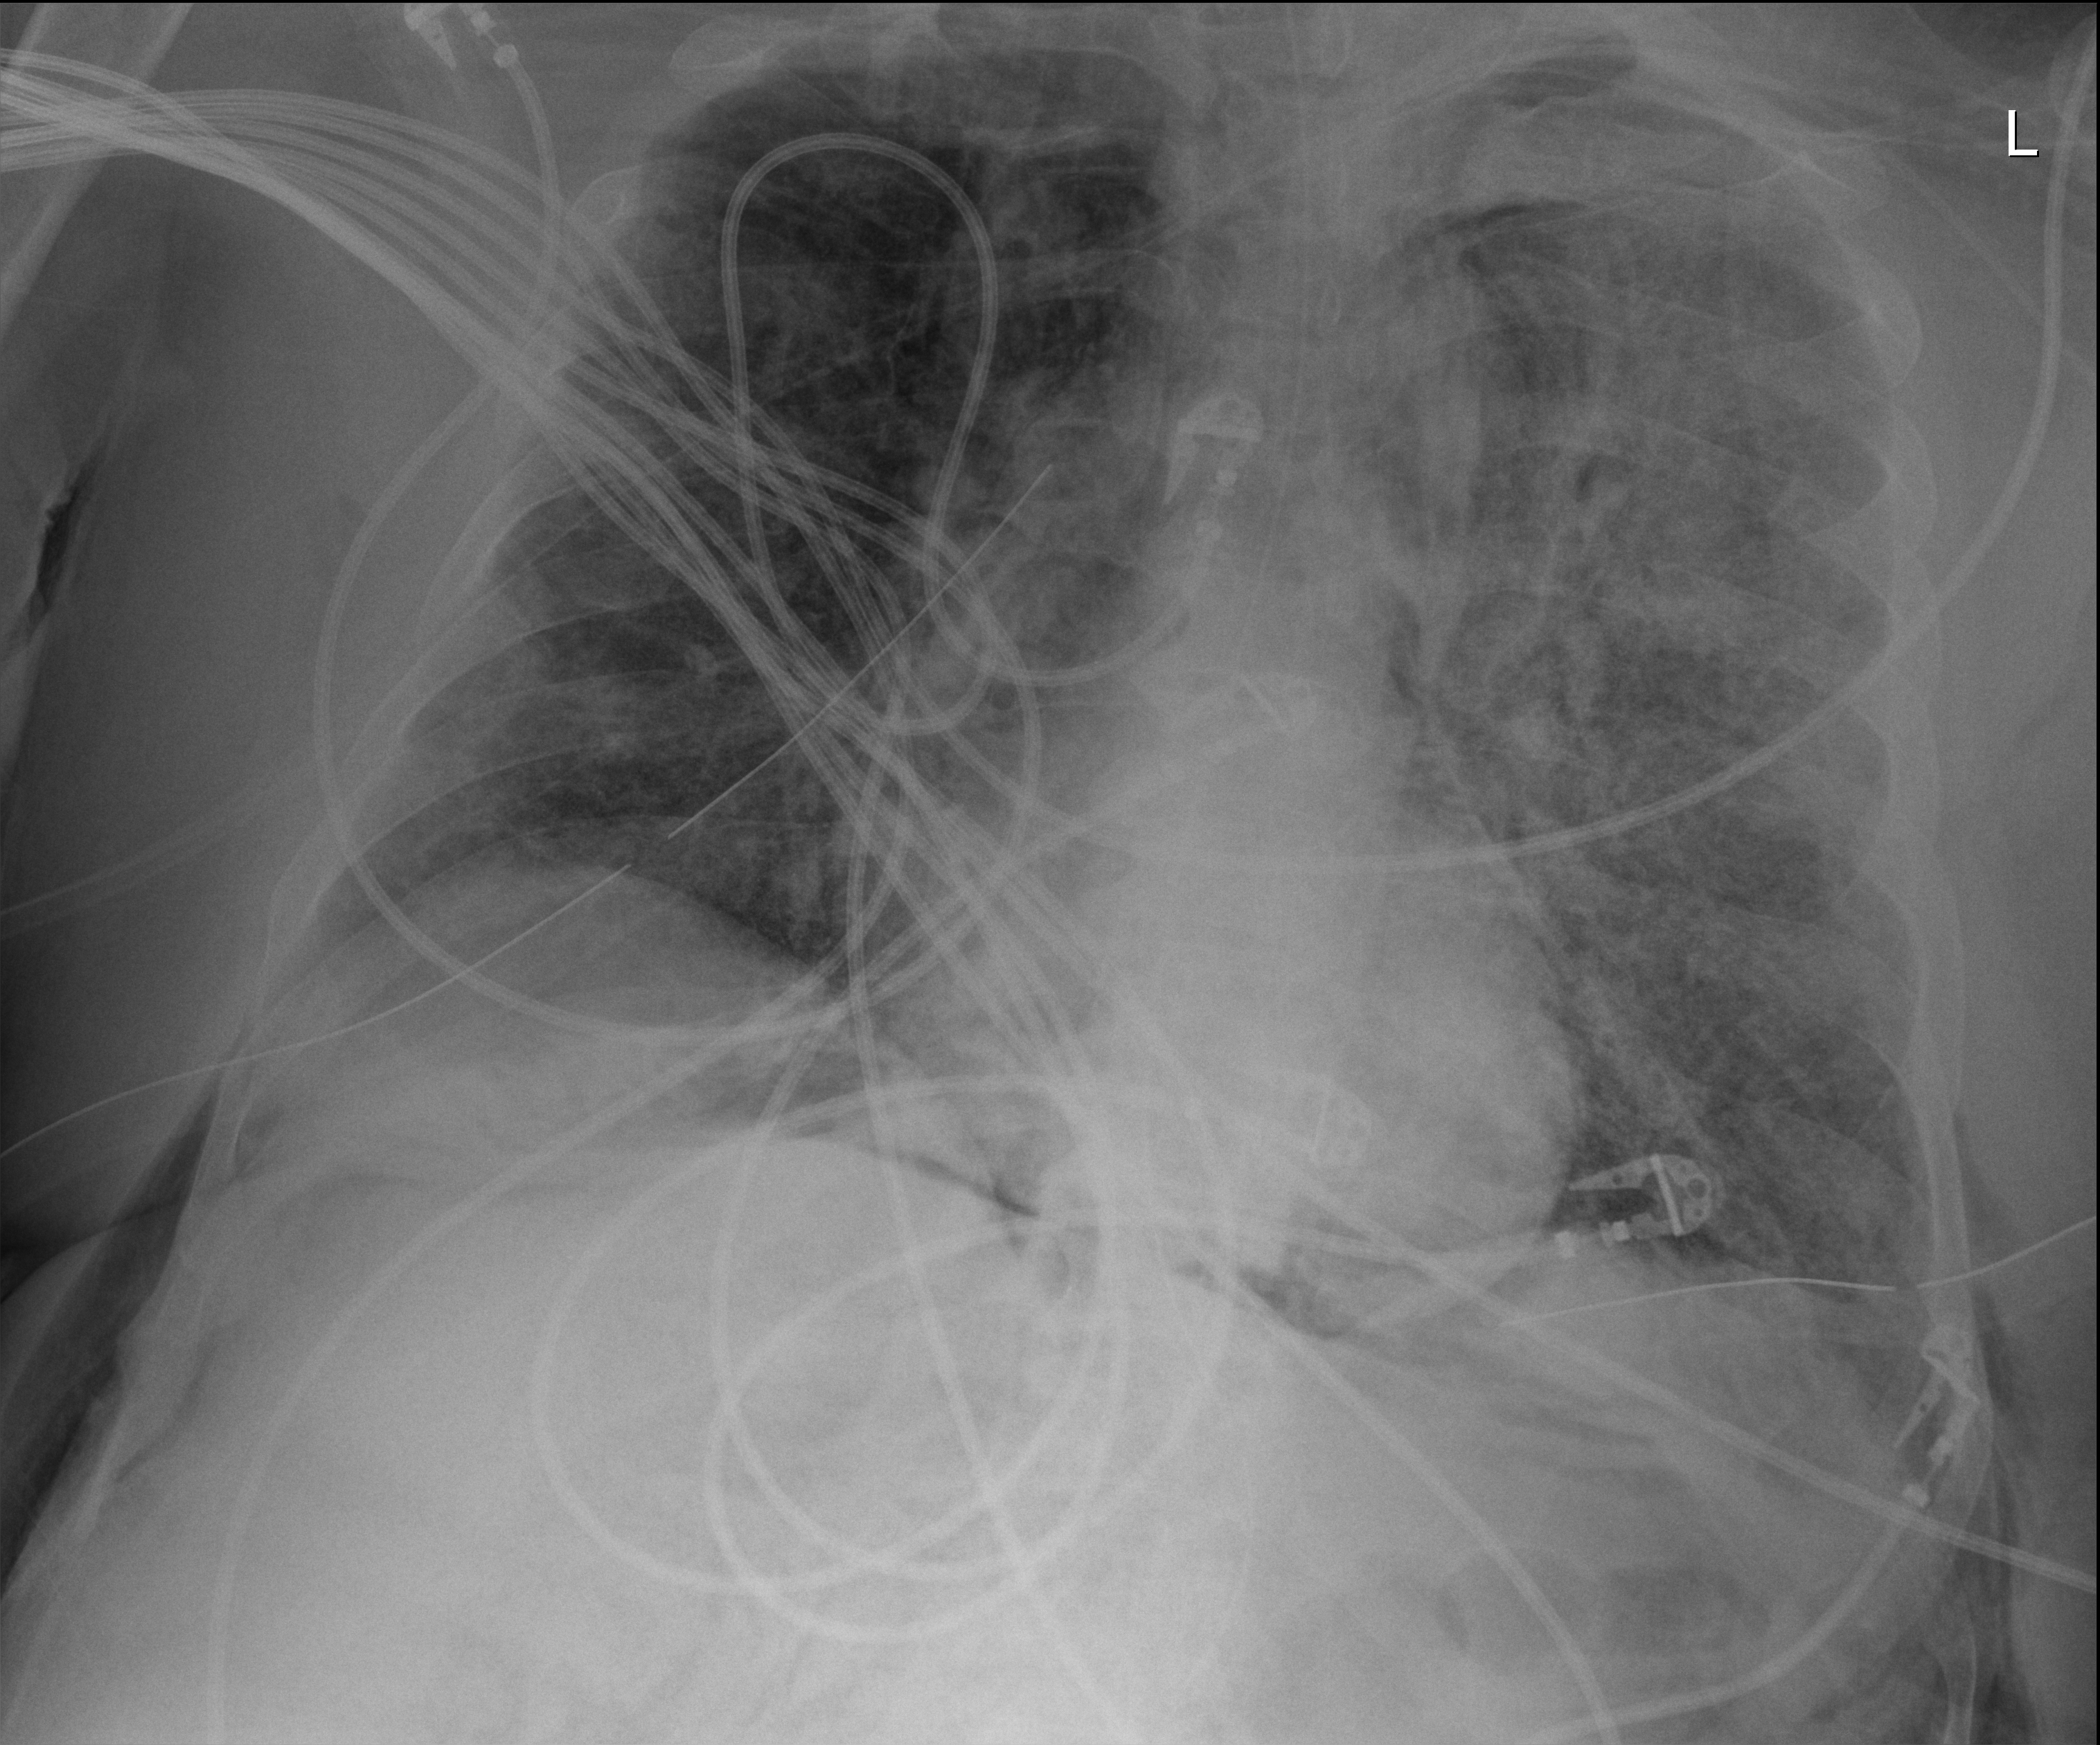
Portable chest radiograph, anteroposterior (AP) projection. Patient hospitalised with COVID-19, aged 18–59 years.
Hospital-stay facts (about this admission, not read from this image; timing relative to this image not recorded):
- other chronic lung disease (admission record): no
- COPD (admission record): no